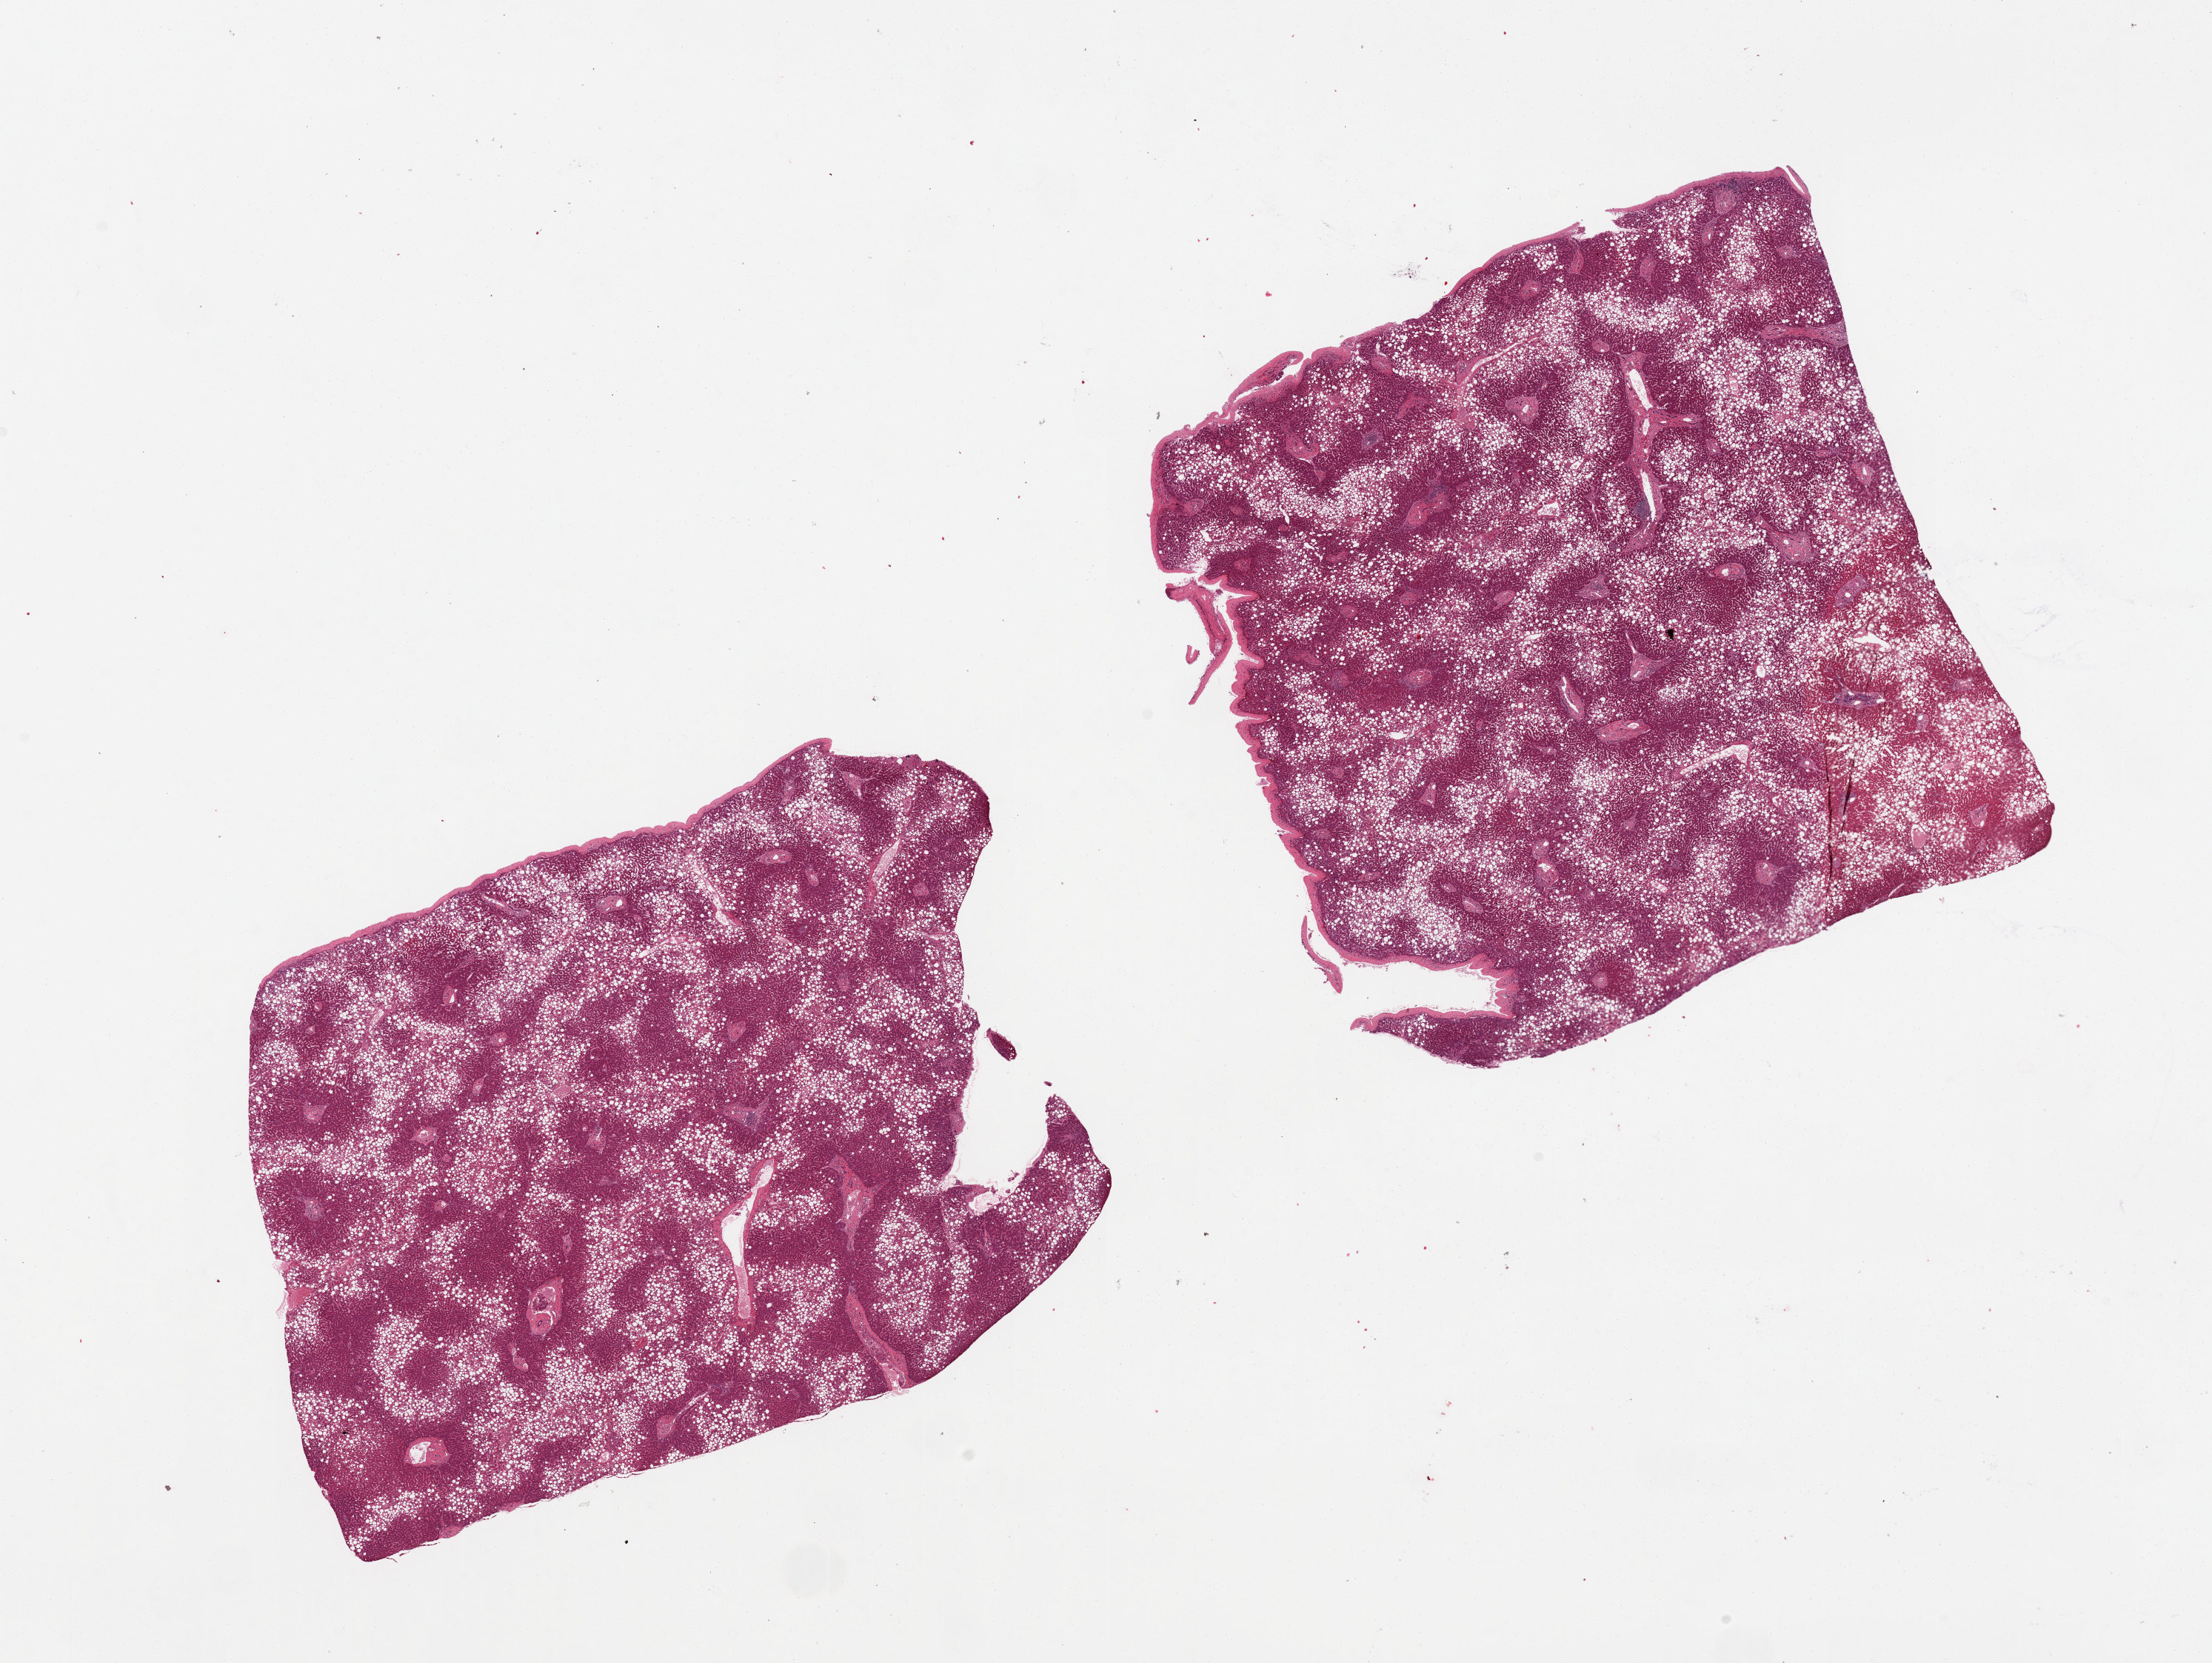
Digitized hematoxylin and eosin (H&E)-stained section — a low-resolution overview of the entire scanned area, about 23.6 x 17.8 mm (acquisition: 20x scan). PAXgene-fixed paraffin-embedded (PFPE) section. Section of liver (target tissue). Donor tissue sample. Male donor.
Reviewer comment on this tissue sample: 2 pieces; diffuse macrovesicular steatosis involving about %60 of the liver parenchyma, few collections of chronic inflammatory cells.